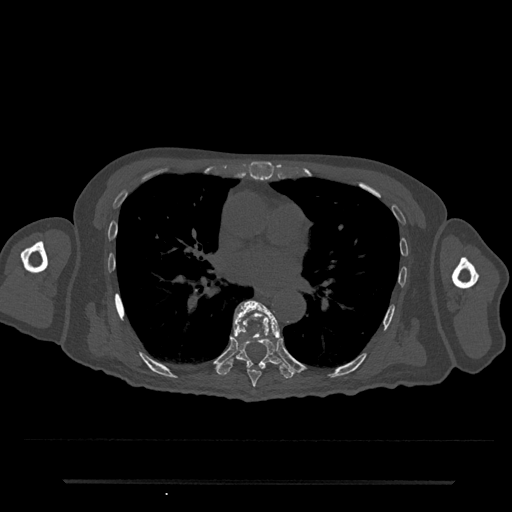
CT including the spine, one axial slice. Reconstruction kernel Br40s/3. 120 kVp. Bone window (W 1800 / L 400 HU). 512 × 512 image matrix, field of view 427 × 427 mm. Male patient, age 74 years. From the clinical record (not read from this slice): primary cancer: prostate.
Annotated regions visible in this slice (semi-automatic segmentation, software-assisted and operator-edited):
- T7 vertebra: bounding box <233,301,280,388> (left, top, right, bottom; pixels)
- T8 vertebra: <216,300,294,379>